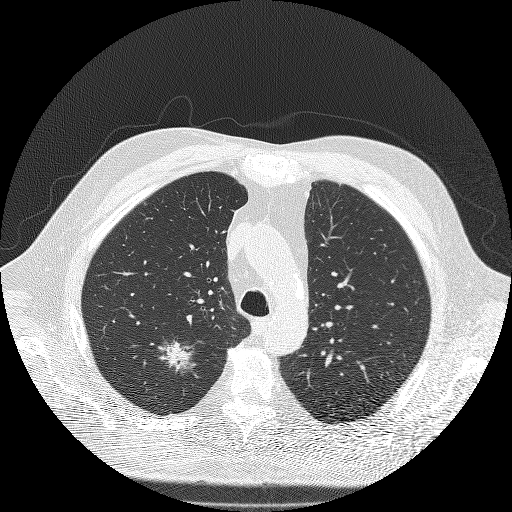
Axial slice from a low-dose chest CT screening exam; second screening round (one year after baseline); lung window (W 1500 / L -600 HU); 2 mm slice thickness; lung (sharp) reconstruction kernel (FC51); 512 × 512 image matrix. Male, age 71 years at enrolment. Former smoker at enrolment.
Expert-annotated lung lesion, bounding box (x1, y1, x2, y2) in pixels: (137, 326, 205, 389). The screening reader recorded 3 non-calcified nodules or masses ≥4 mm on this exam (right upper lobe, right upper lobe, right lower lobe); which of them this box marks is not recorded. Later outcome: lung cancer diagnosed 59 days after this screen — bronchiolo-alveolar adenocarcinoma, NOS, right upper lobe, moderately differentiated (G2), stage IIIA (AJCC 6th edition), 25 mm at pathology.